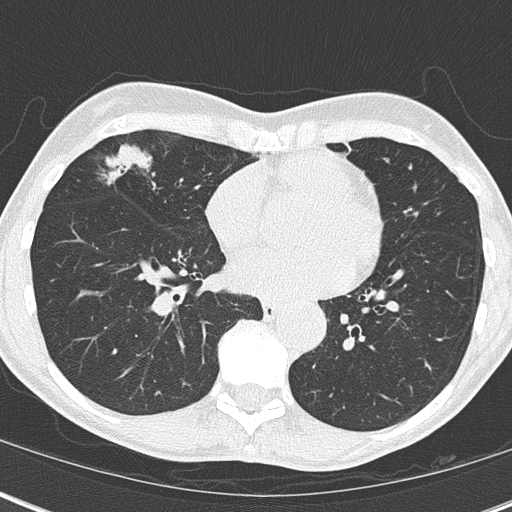
Chest CT (low-dose screening protocol), one axial image, third annual screen, lung window (W 1500 / L -600 HU), lung (sharp) reconstruction kernel (B50f), slice 104 of 173 in the series, 512 × 512 image matrix, field of view 290 × 290 mm. Female, age 67 years at enrolment. Current smoker at enrolment.
- Lesion marked by an expert reader, bounding box (x1, y1, x2, y2) in pixels: (92, 140, 190, 225).
- The exam's reader record, not a measurement of the box and not confirmed to be the same lesion: non-calcified nodule or mass ≥4 mm, right middle lobe, 32 × 17 mm, mixed attenuation, pre-existing on the prior screen: yes; interval growth: yes.
- Official screen result: positive, other.